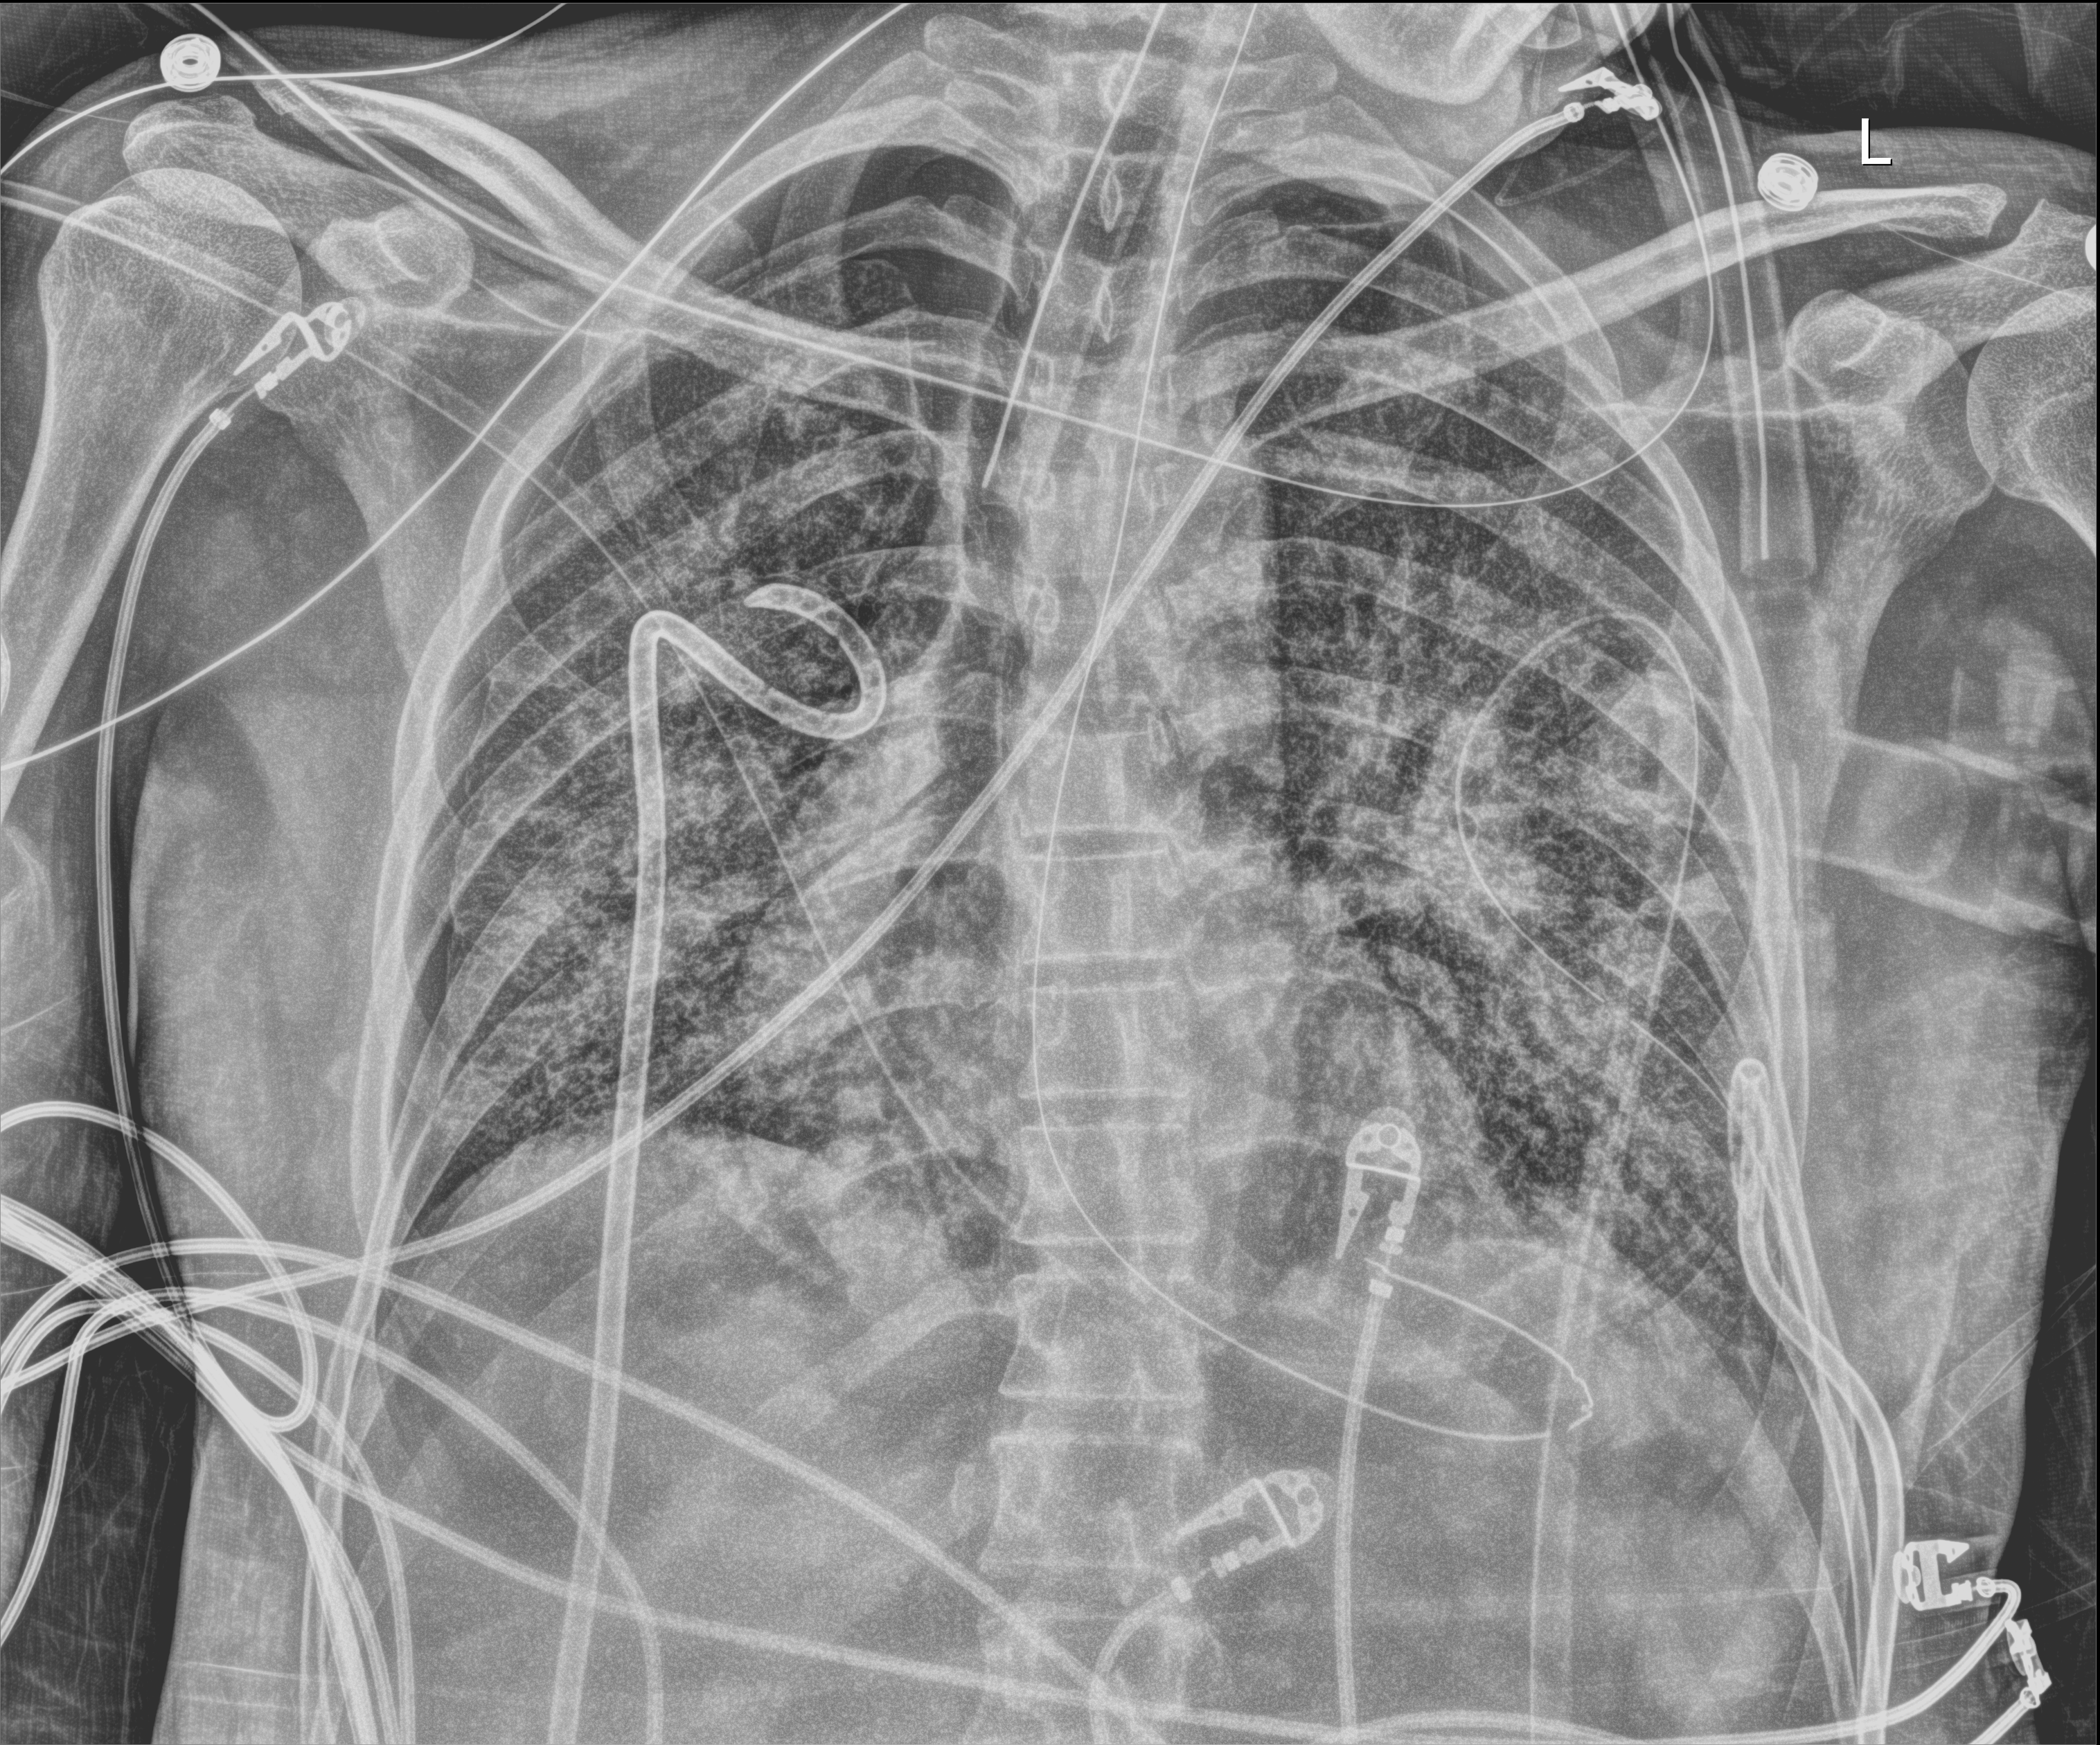
Chest X-ray. Patient hospitalised with COVID-19, aged 18–59 years.
From the hospital-stay record, not from the radiograph (when in the stay this image was taken is not recorded):
- admitted to intensive care during this hospital stay: yes
- hypertension (admission record): no